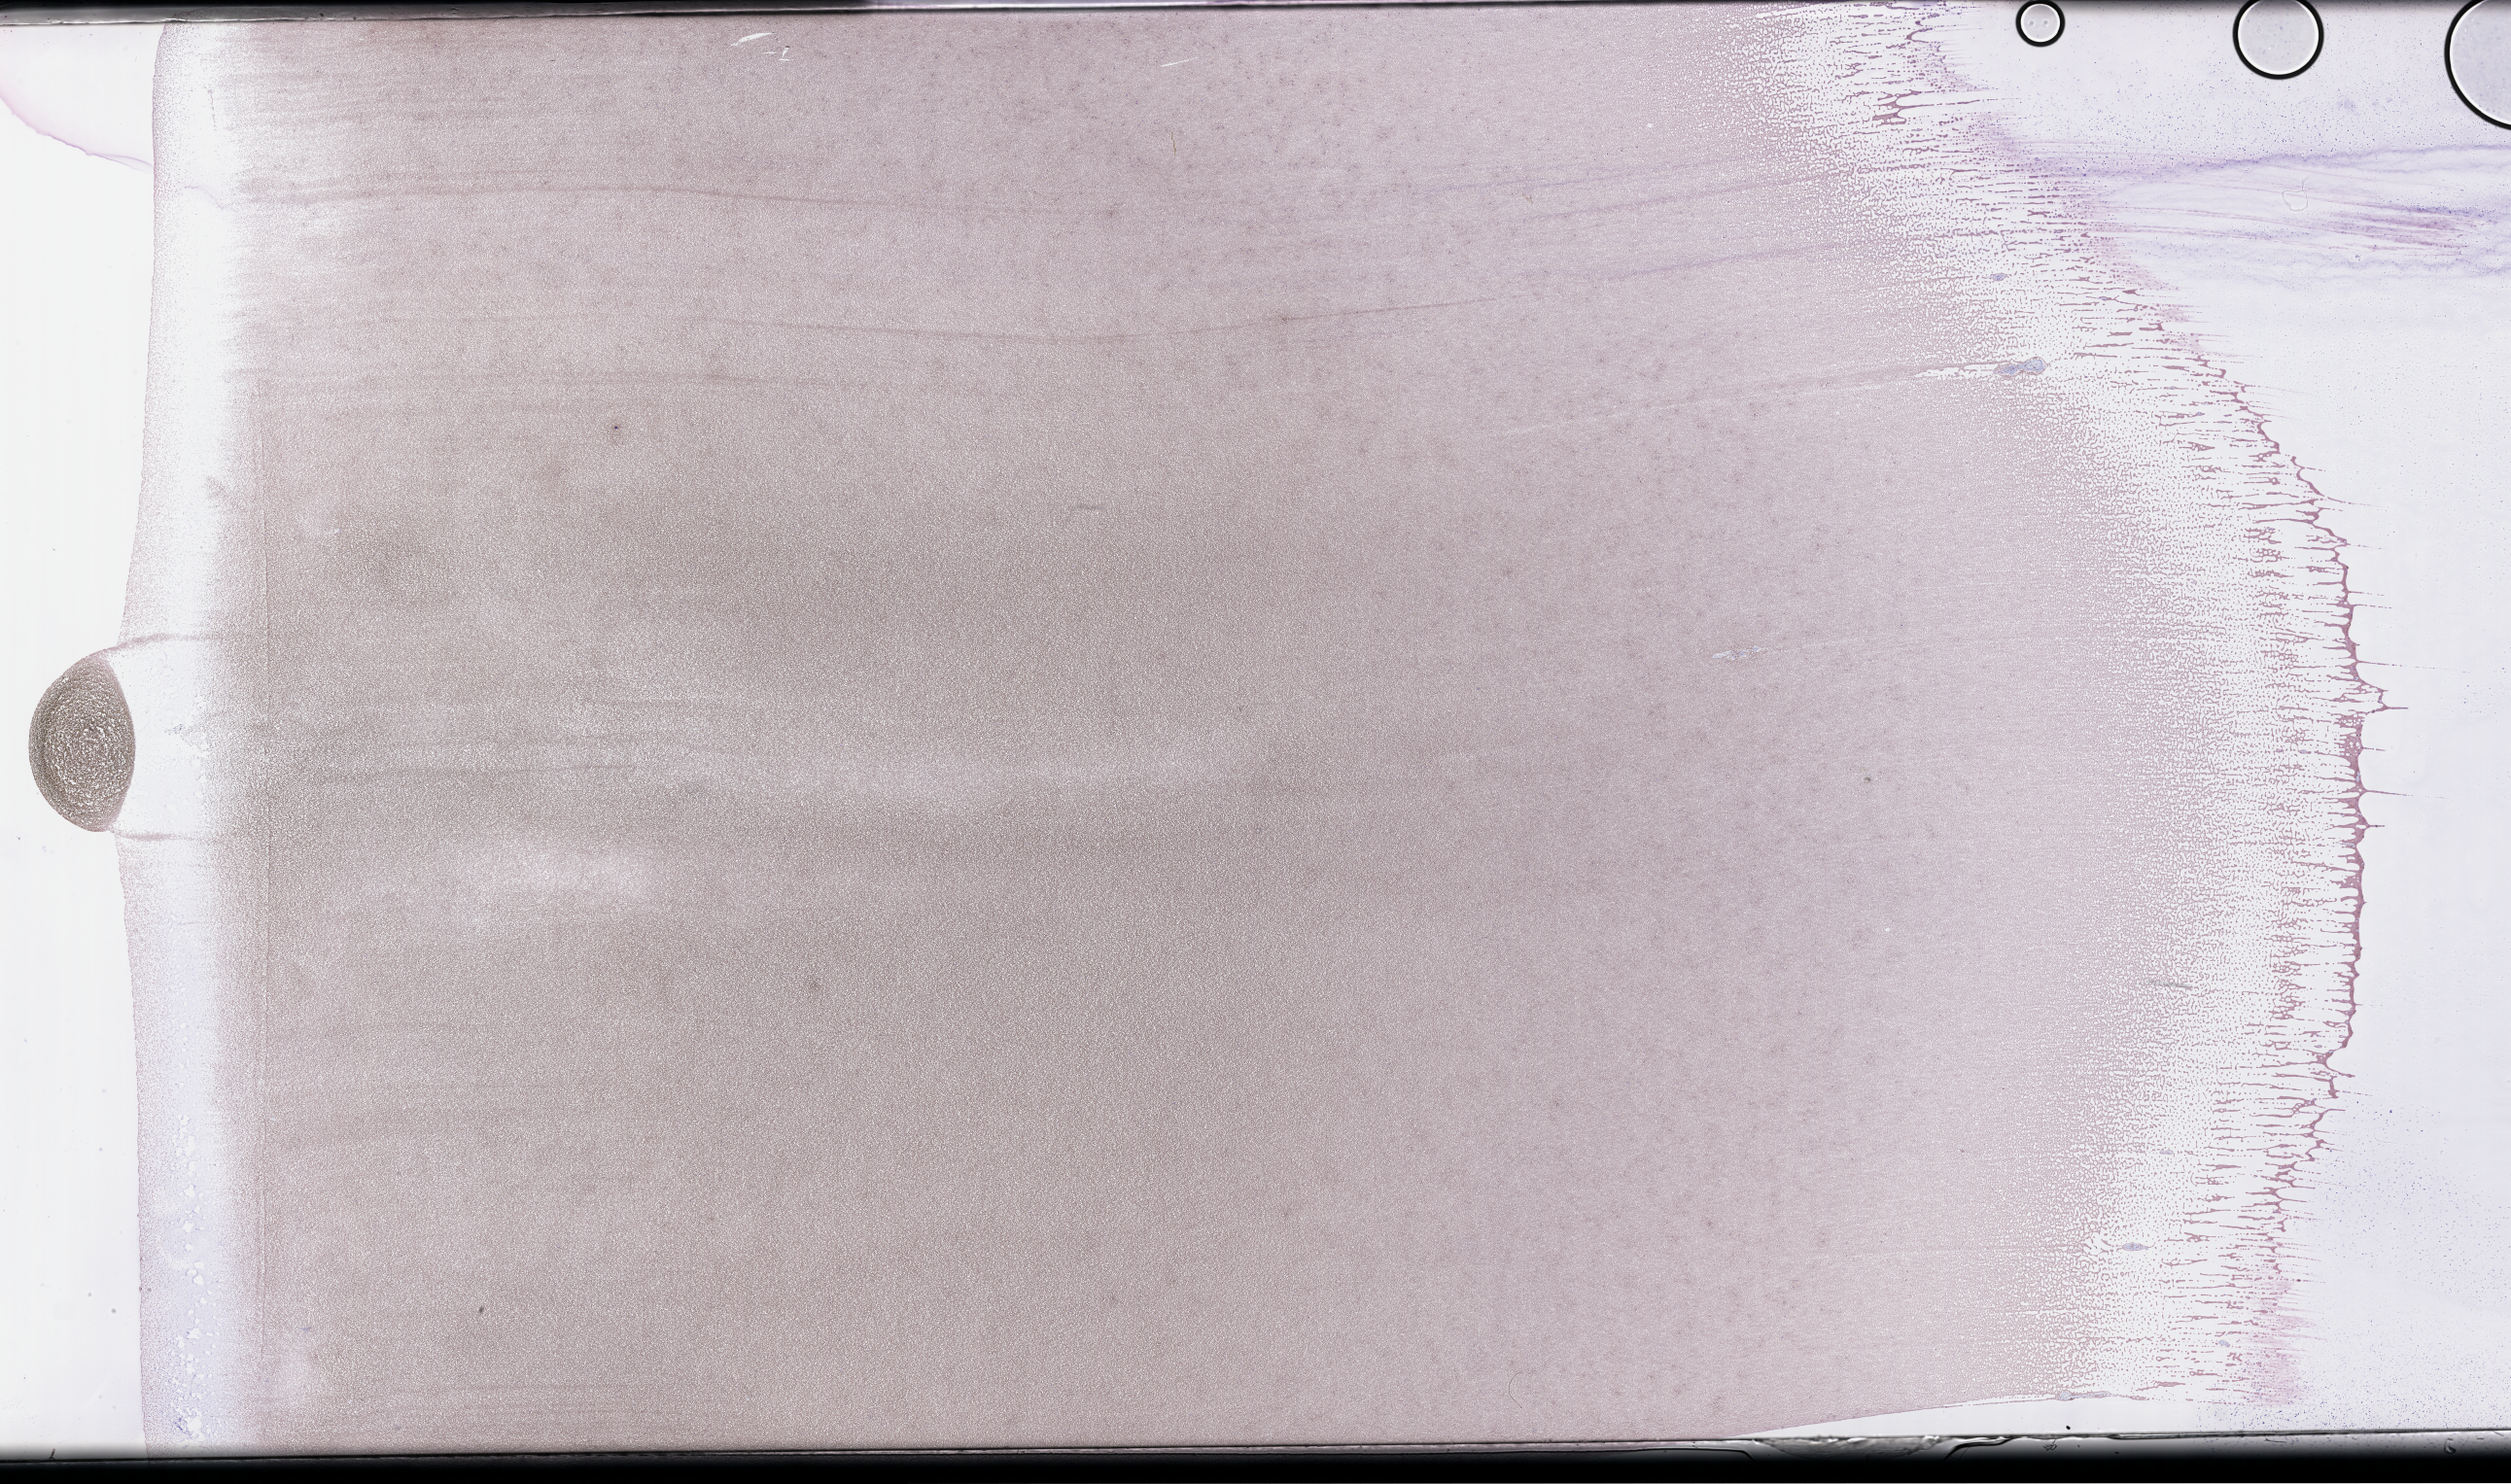
Whole-slide image of a whole blood smear, Wright-Giemsa stain — shown as a low-resolution overview of the whole scanned area (about 41.7 x 24.7 mm). Specimen time point: collected at baseline (before treatment). Patient sex: female.
From a patient with: Plasma Cell Myeloma.